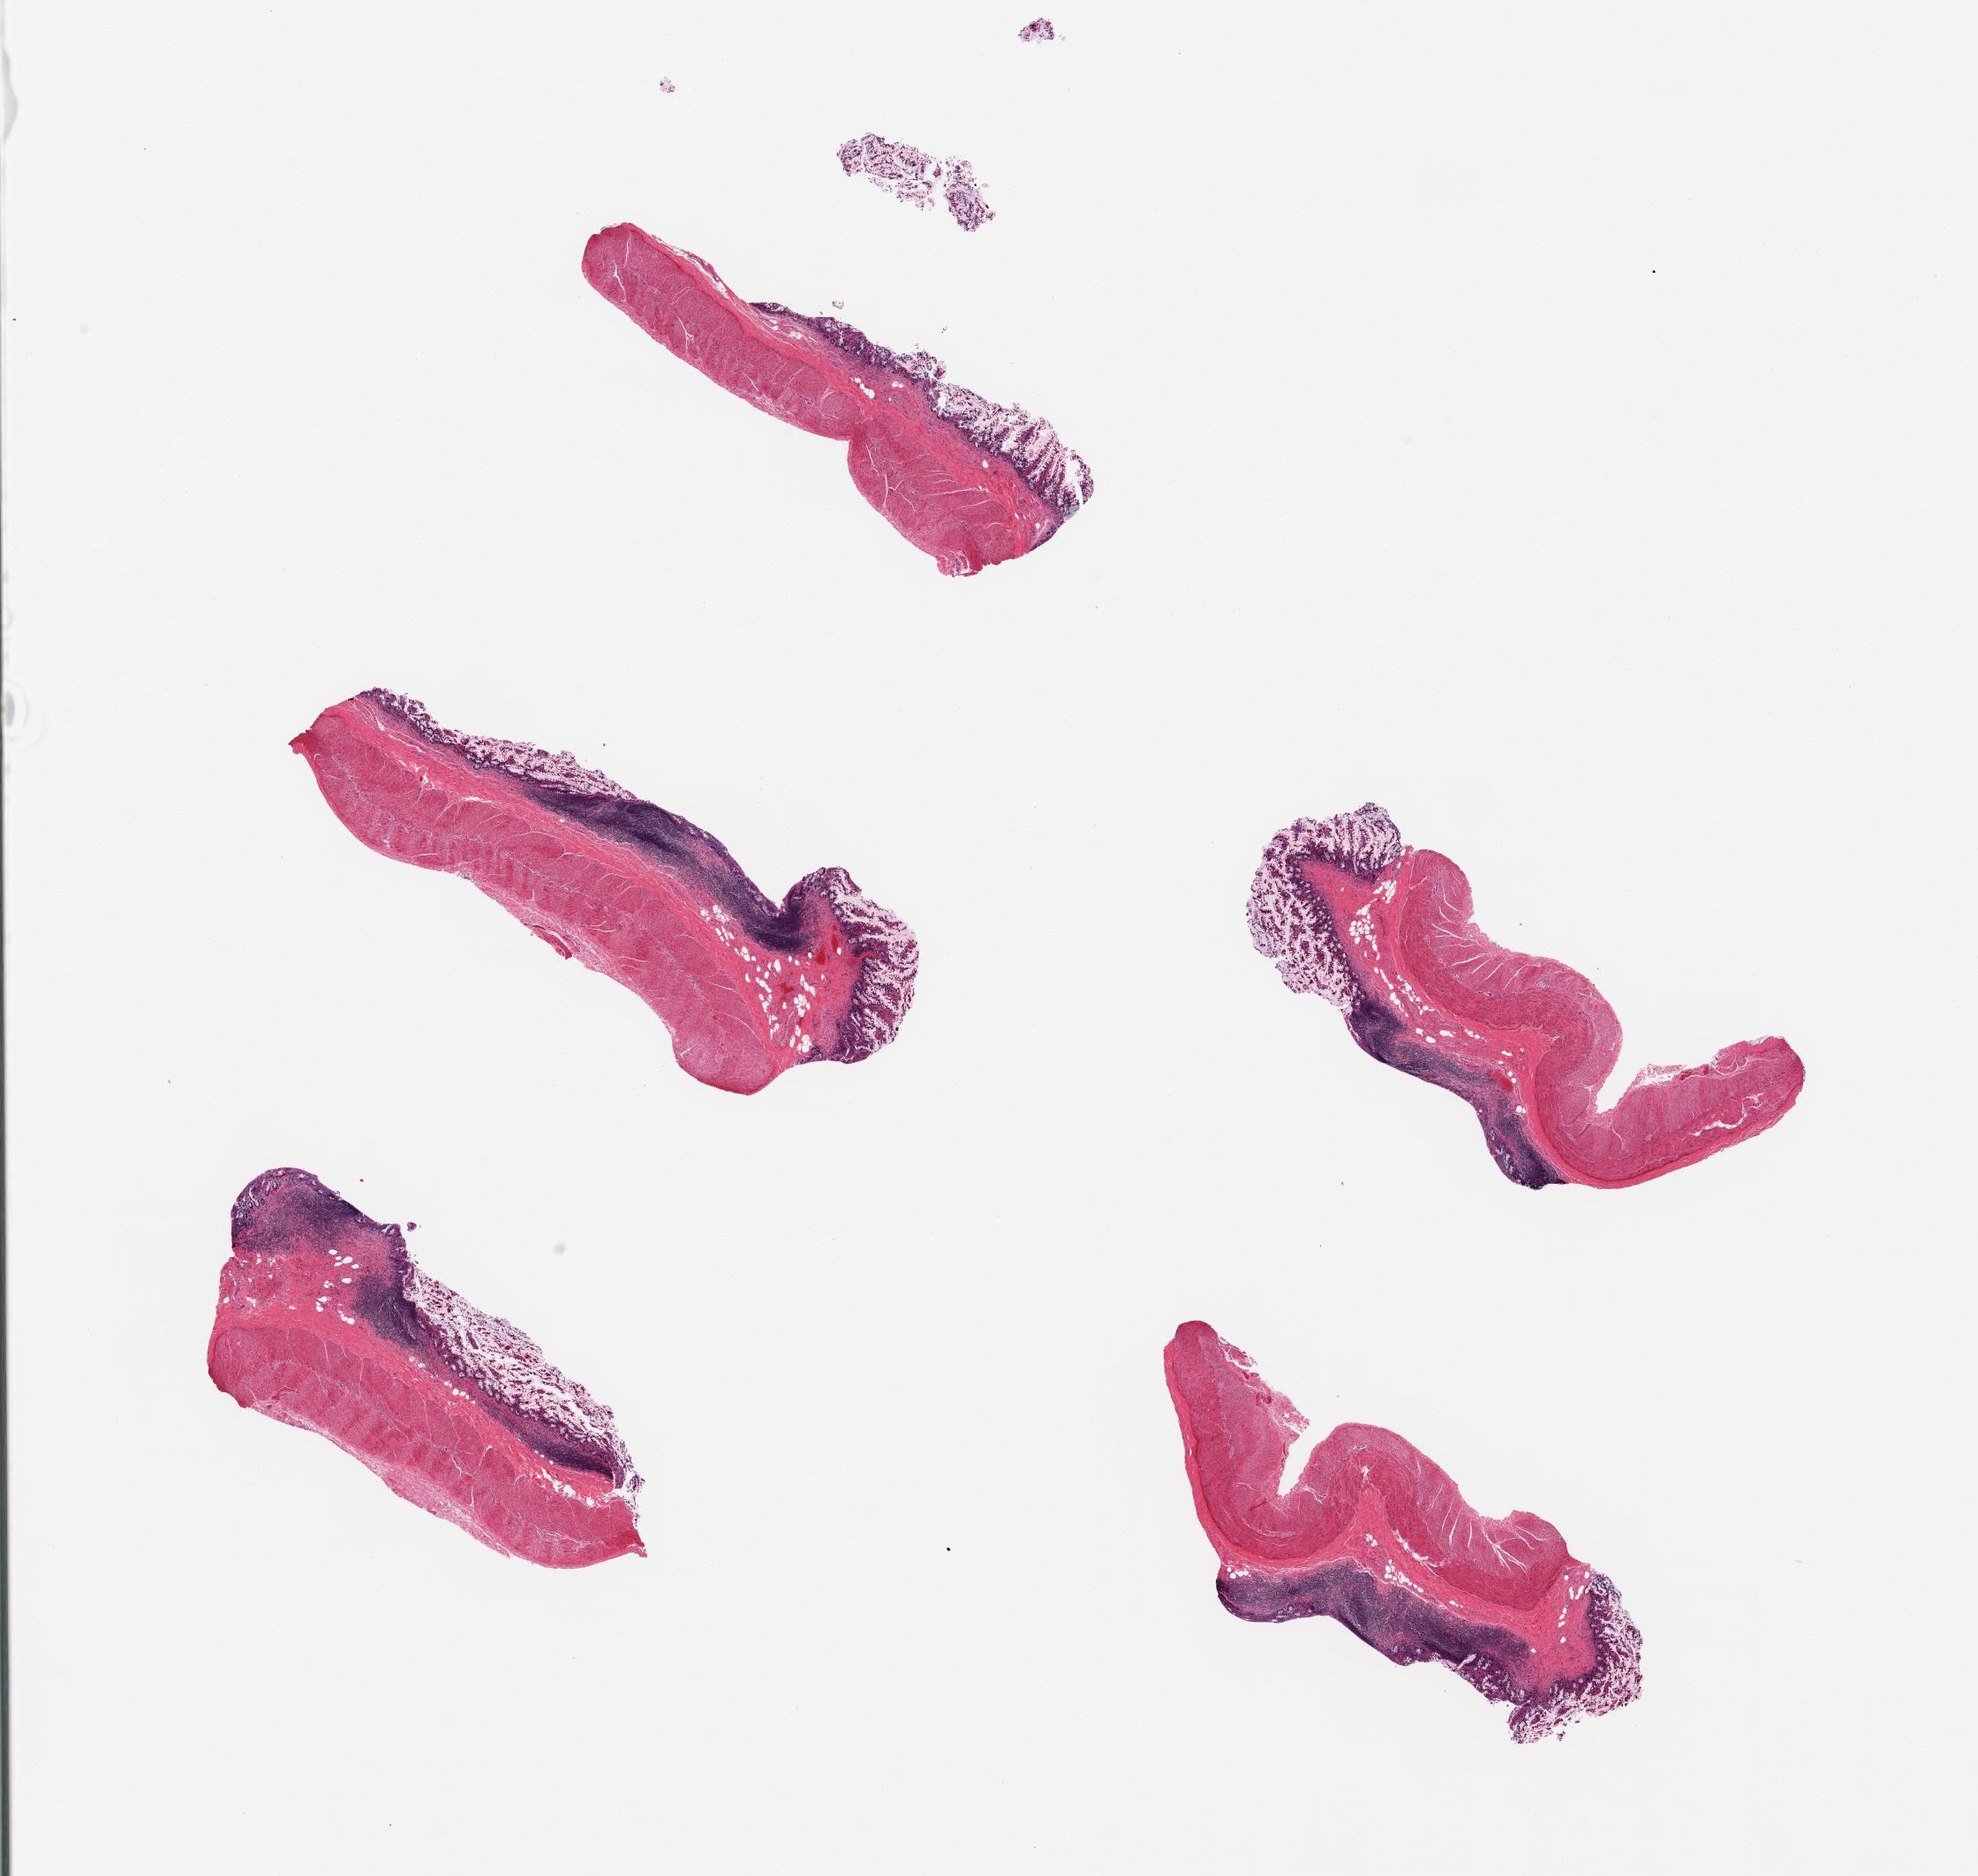
Digitized H&E-stained section — shown as a low-resolution overview of the whole scanned area (about 17.7 x 16.8 mm, slide scanned at 20x).
Specimen: PAXgene-fixed, paraffin-embedded tissue; target tissue: ileum; donor tissue sample.